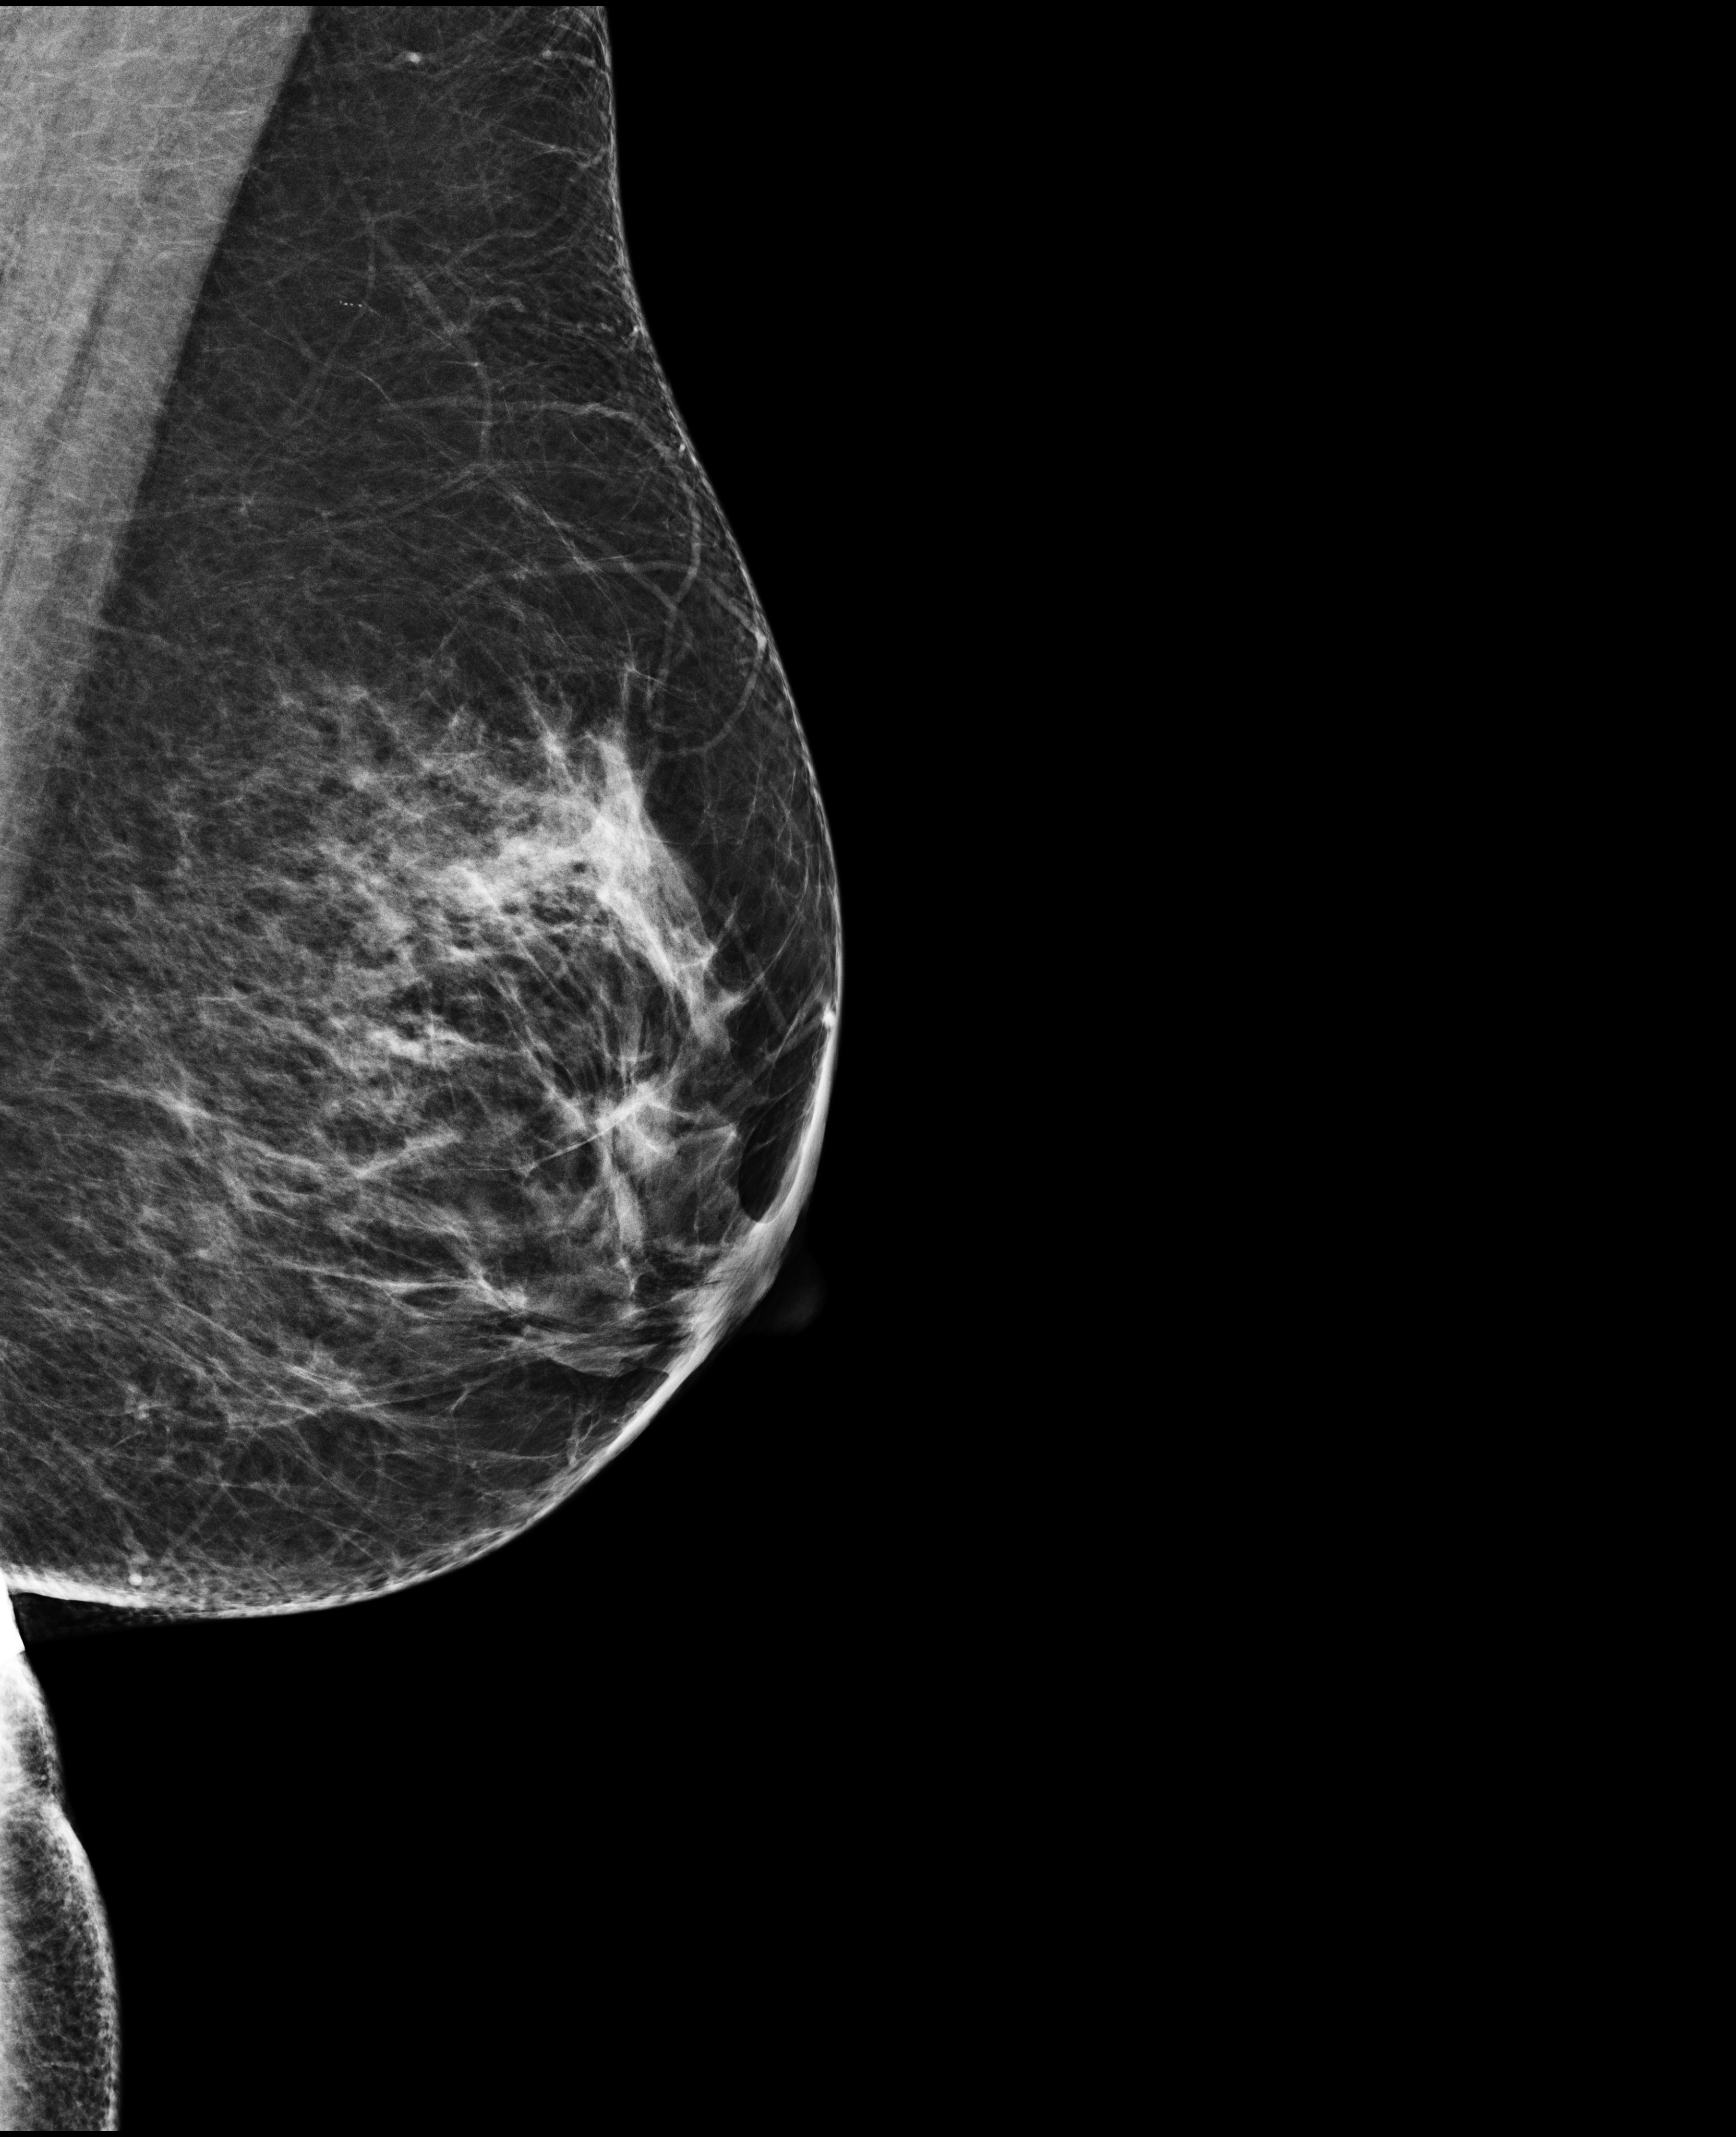
Digital mammogram (FFDM); left breast; medio-lateral oblique projection; screening examination; compressed breast thickness 60 mm; system: Selenia Dimensions. Female patient, age 56 years.
Breast density at the screening exam (both breasts): heterogeneously dense (BI-RADS density category c). Final BI-RADS category for the screening round (tomosynthesis exam, both breasts): category 1. Recall: recalled for additional imaging after this screen.